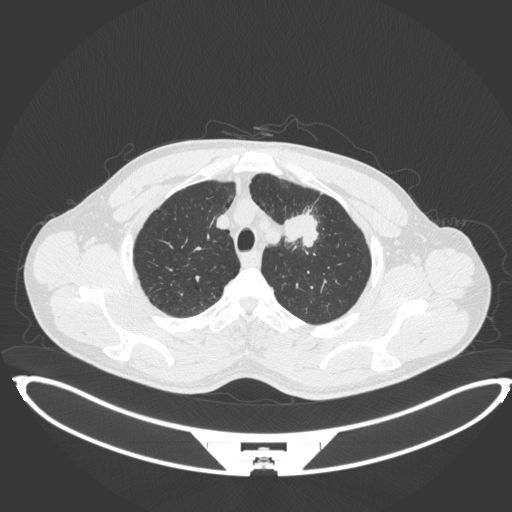
Chest CT, one axial slice. Slice 361 of 407 in the series (ordered by position). Lung window (W 1500 / L -600 HU). 512 × 512 image matrix, field of view 457 × 457 mm. Male patient, age 60 years. Case-level facts recorded for this patient, not image findings: clinical TNM (as recorded): T2a N0 M0.
Annotated regions visible in this slice (bounding box drawn by a radiologist):
- lung tumour (recorded histology: squamous cell carcinoma): bounding box <283,212,320,249> (left, top, right, bottom; pixels)